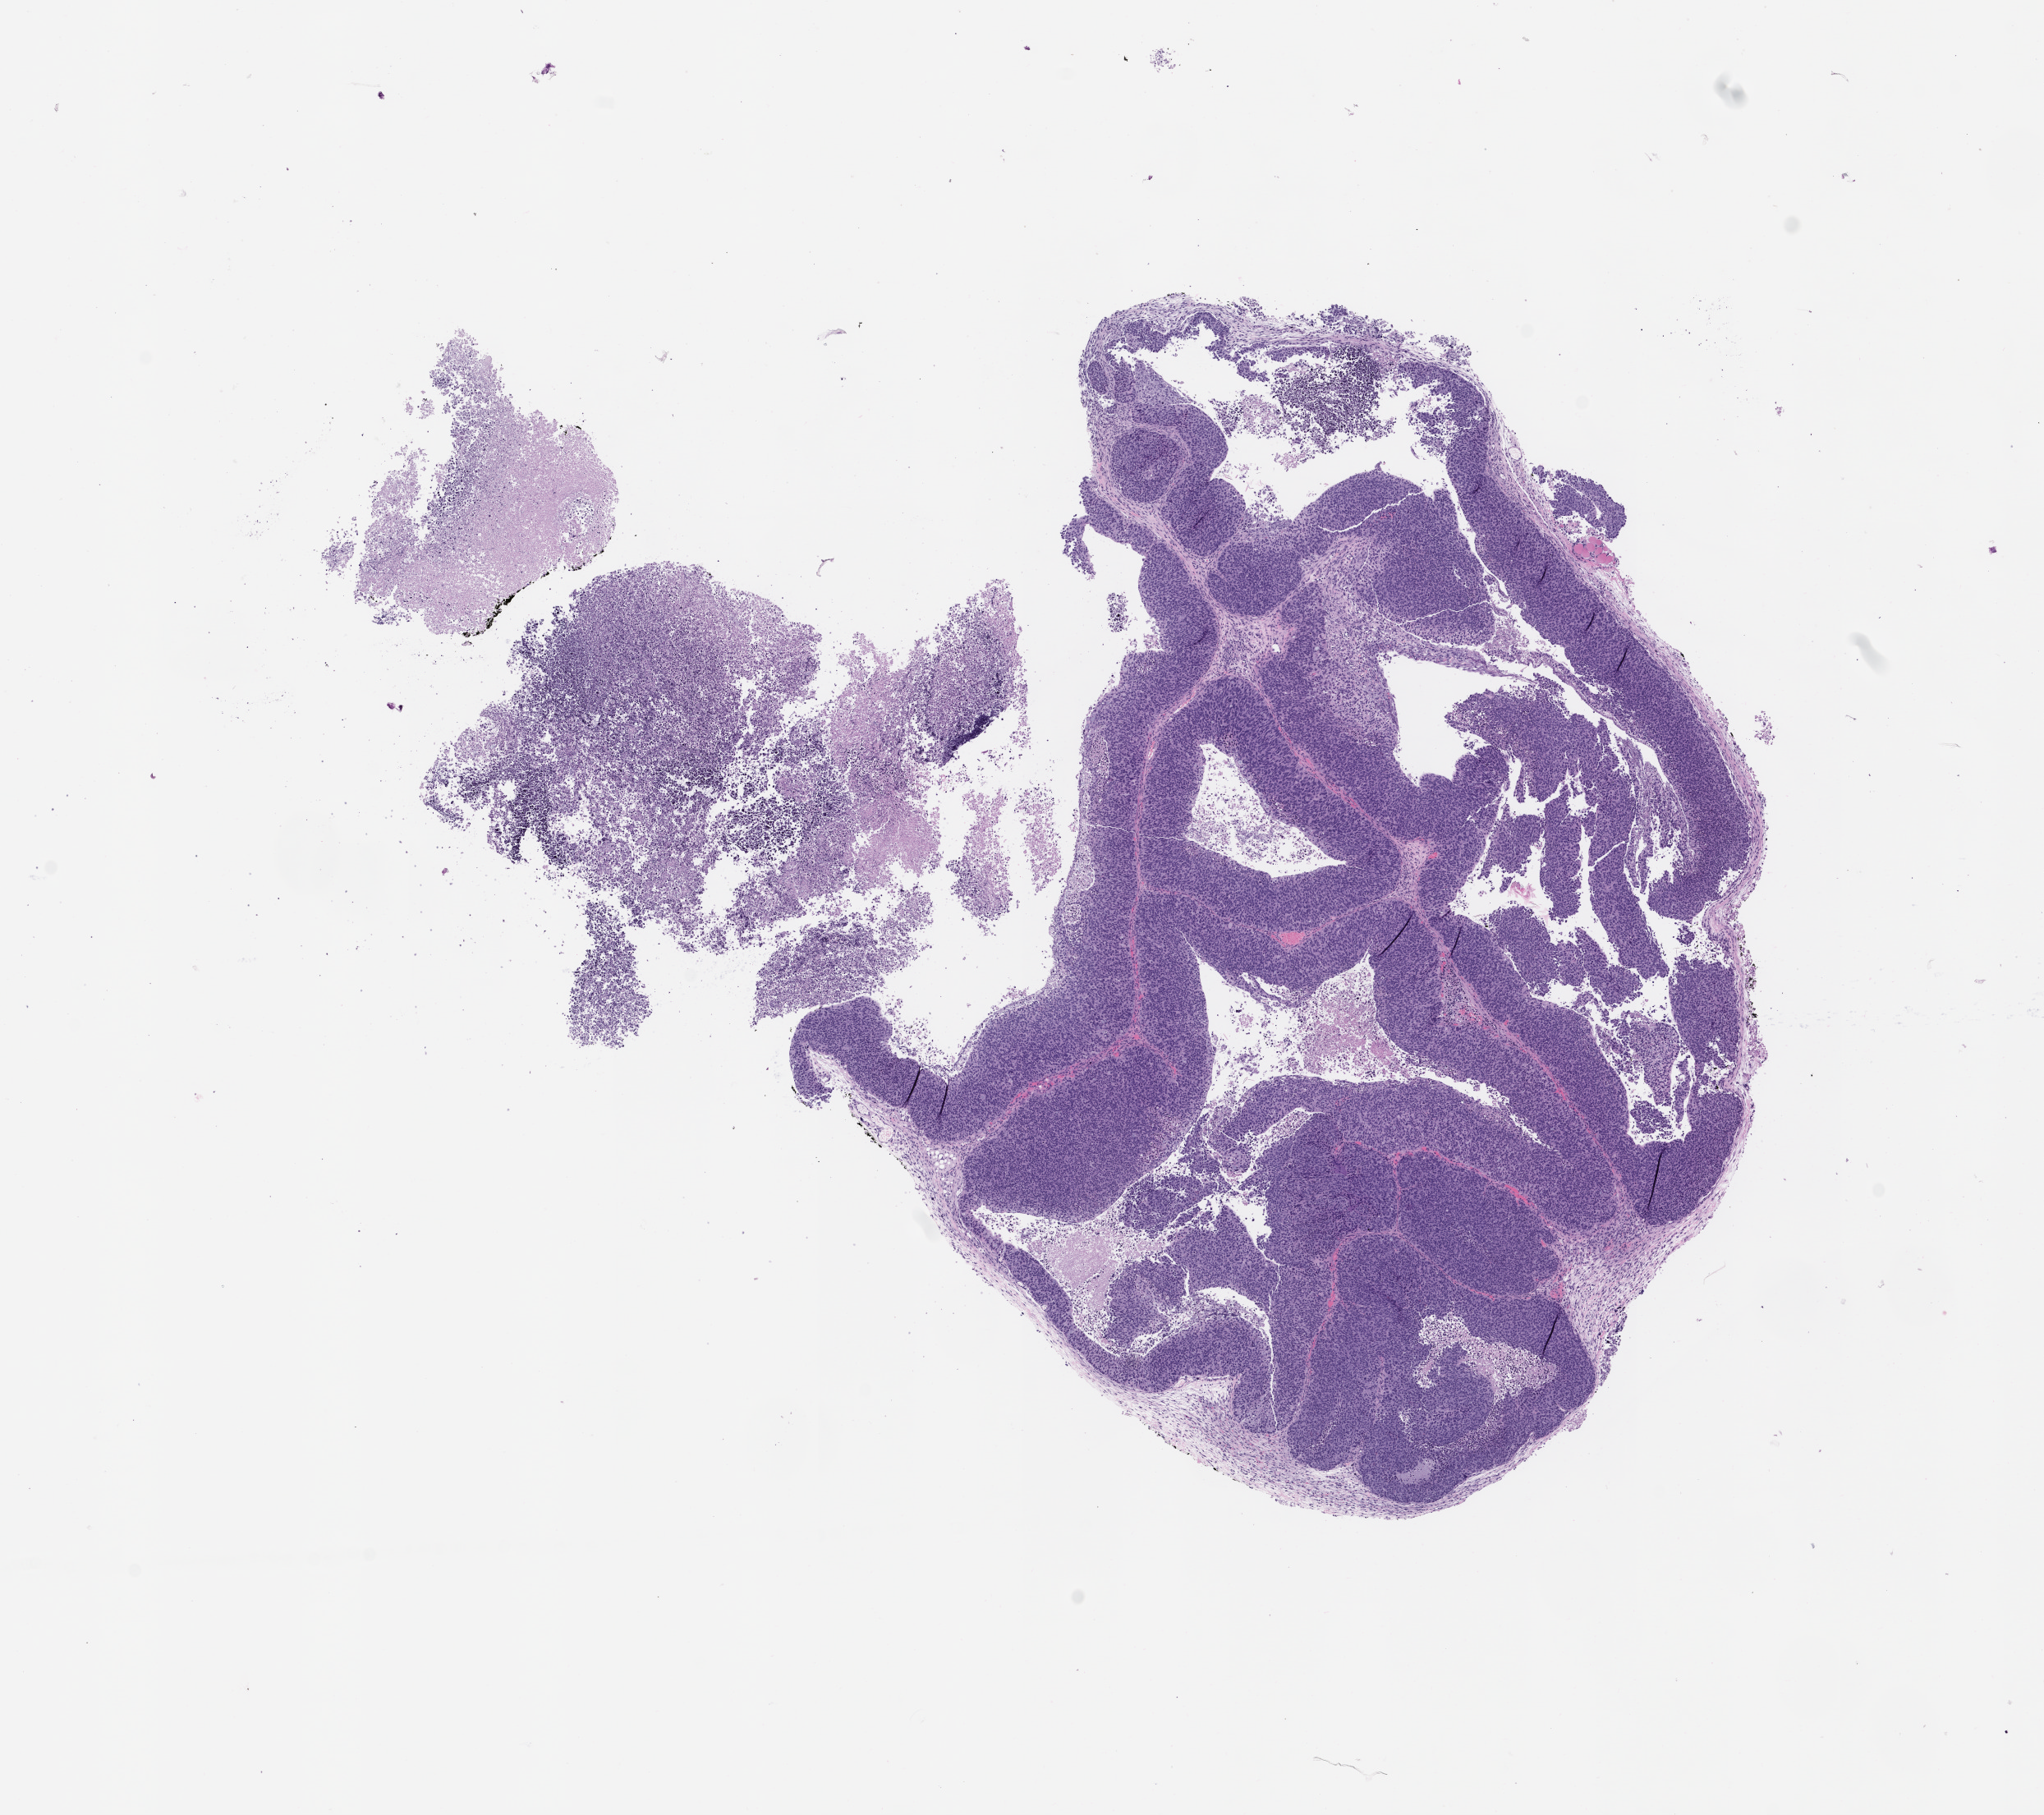
H&E whole-slide image of a patient-derived xenograft (PDX) tumor grown in a mouse, passage 2 — shown as a low-resolution overview of the whole scanned area (about 10.0 x 8.9 mm); formalin-fixed paraffin-embedded section; tumor site category: gastrointestinal tract.
Originating patient diagnosis: Gastric Adenocarcinoma.